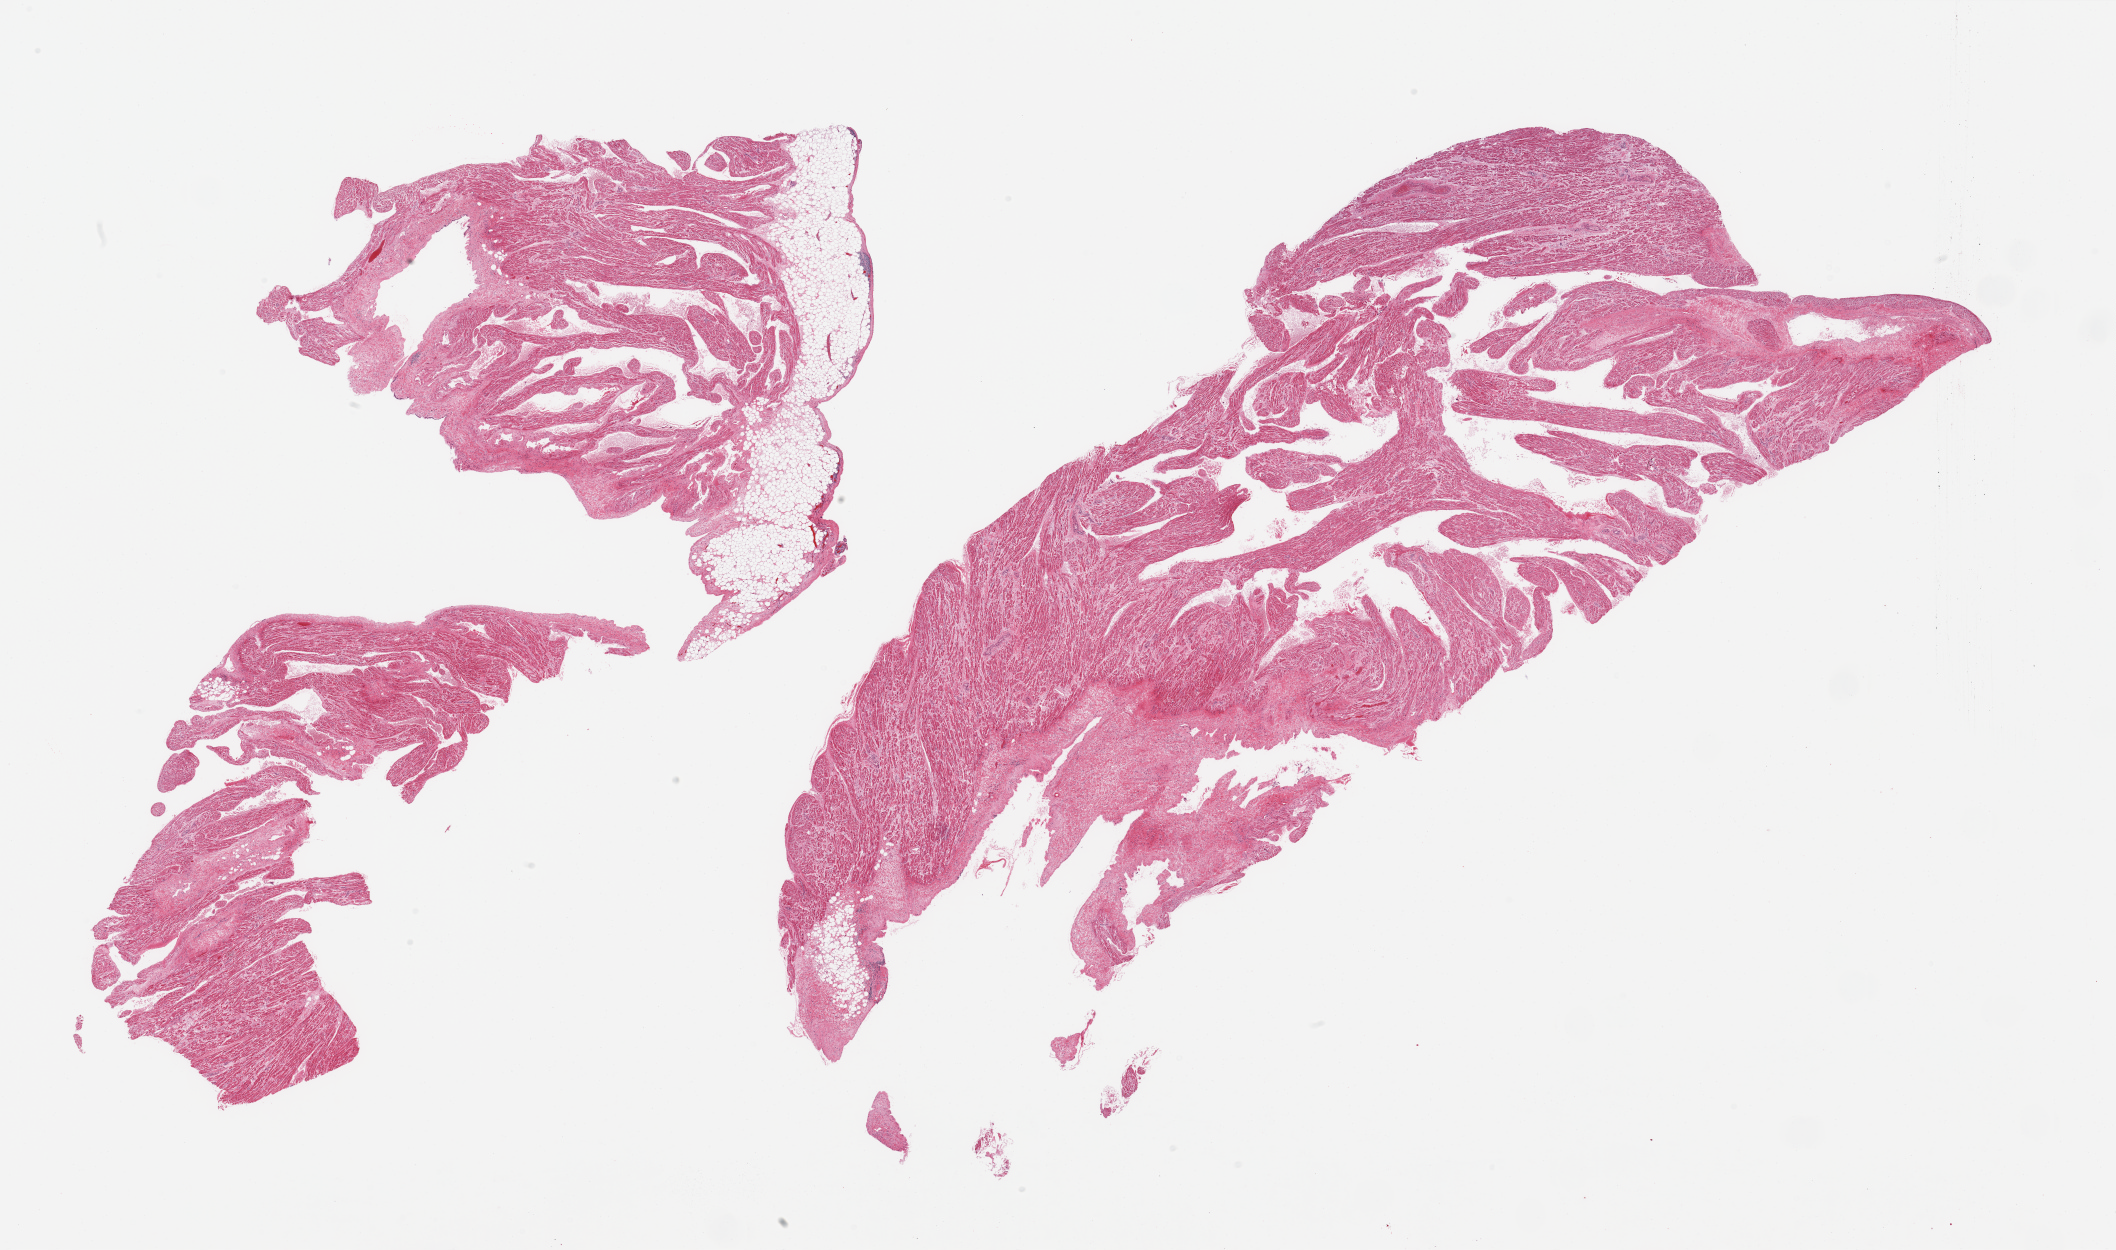
Hematoxylin and eosin (H&E) whole-slide image, brightfield — a low-resolution overview of the entire scanned area, about 33.5 x 19.8 mm; PAXgene-fixed, paraffin-embedded tissue; section of auricular appendage (target tissue); donor tissue sample. Male donor.
* pathologist's review note for this sample: 3 pieces; 1 with 7x1.4mm external fat